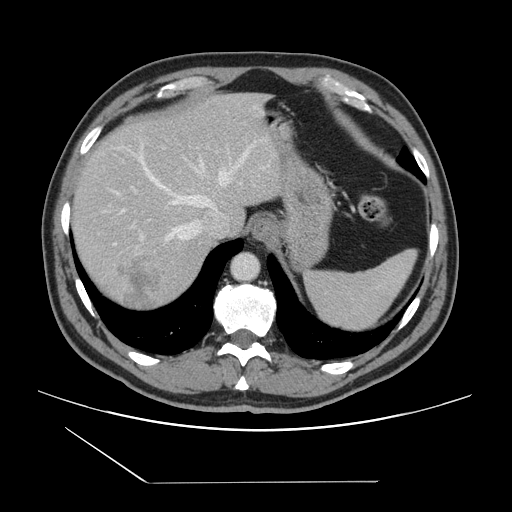
Contrast-enhanced abdominal CT, one axial slice. Position 118 of 157 along the scan axis. 120 kVp. Intravenous contrast given. Soft-tissue window (W 400 / L 40 HU). 2.5 mm slice thickness. 512 × 512 image matrix. Male patient, age 61 years. Case-level facts recorded for this patient, not image findings: diagnosis: colorectal cancer liver metastases, imaged before liver resection; multiple liver metastases: yes; largest metastasis: 5.5 cm; disease in both lobes: yes.
Structures marked on this image (outlined manually by an expert reader):
- hepatic veins: bounding box [x1, y1, x2, y2] px = [122, 145, 252, 254]
- liver: [71, 93, 282, 312]
- planned liver remnant (the part of the liver to remain after resection): [72, 94, 235, 232]
- portal vein (with intrahepatic branches): [114, 187, 143, 244]
- liver metastasis: [117, 256, 164, 310]